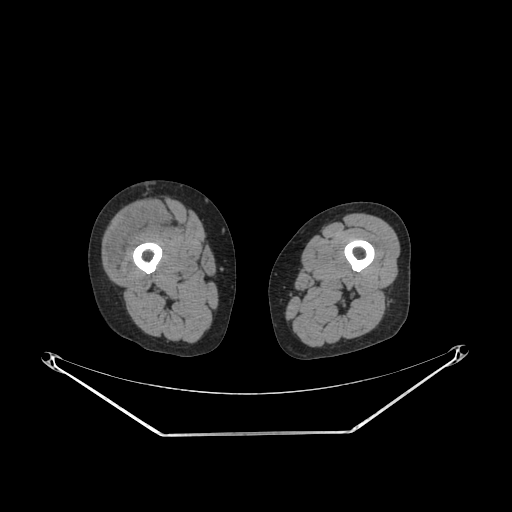
CT of an extremity soft-tissue mass (from a PET/CT study), one axial slice. Slice 221 of 311 in the series (ordered by position). Soft-tissue window (W 400 / L 40 HU). 3.75 mm slice thickness. 512 × 512 image matrix, field of view 500 × 500 mm. Female patient. From the clinical record (not read from this slice): histological type: pleiomorphic undifferentiated sarcoma; grade: high; site of the primary tumour: right quadricep.
Annotated regions visible in this slice (expert contour drawn on MRI and transferred to this co-registered scan by the dataset authors):
- tumour plus oedema (research contour): bounding box <107,205,161,270> (left, top, right, bottom; pixels)